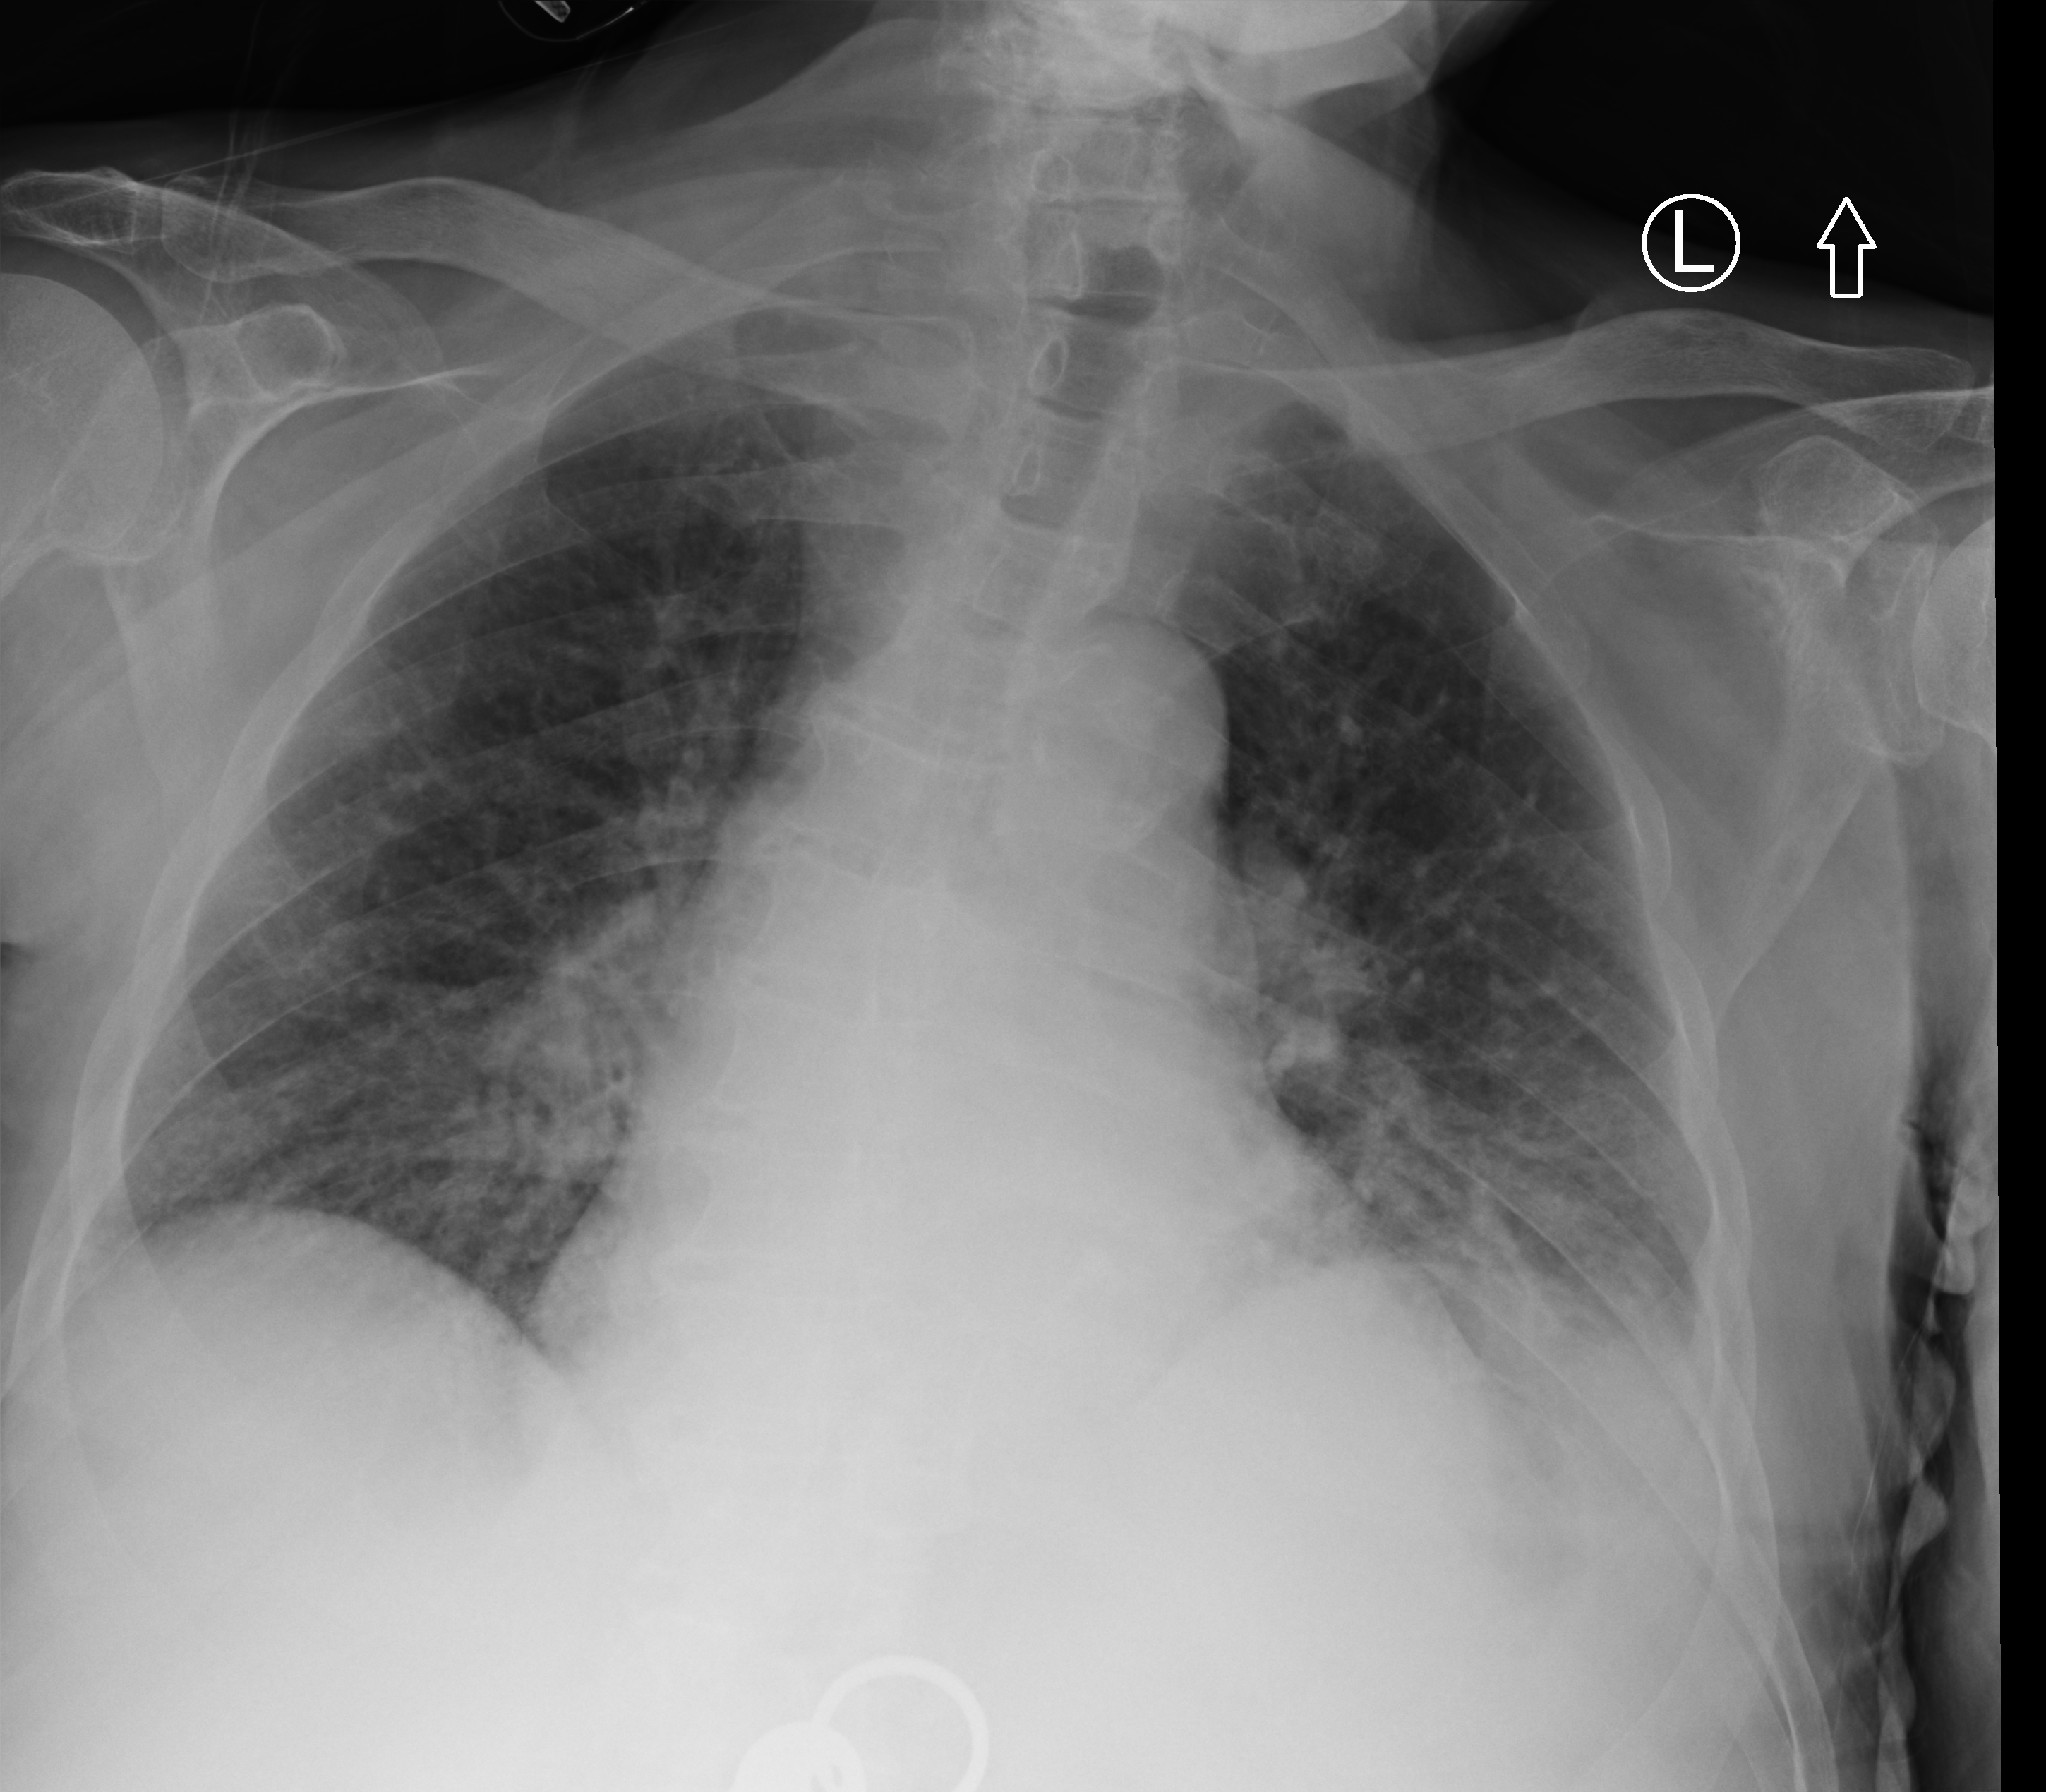
Chest X-ray (portable); anteroposterior (AP) projection. Patient hospitalised with COVID-19; male, aged 75–90 years.
From the hospital-stay record, not from the radiograph (when in the stay this image was taken is not recorded):
- mechanically ventilated during this hospital stay: no